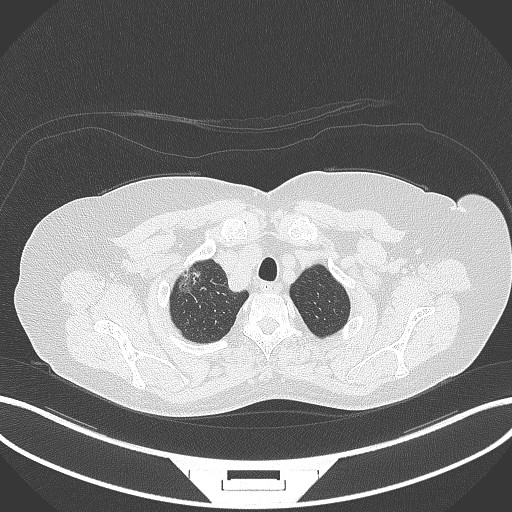
Chest CT, one axial slice; slice 315 of 365 in the series (ordered by position); reconstruction kernel B70f; 120 kVp; lung window (W 1500 / L -600 HU); 1 mm slice thickness; 512 × 512 image matrix, field of view 400 × 400 mm. Female patient, age 62 years. From the clinical record (not read from this slice): clinical TNM (as recorded): T1c N0 M0.
Annotated regions visible in this slice (bounding box drawn by a radiologist):
- lung tumour (recorded histology: adenocarcinoma): bounding box [x1, y1, x2, y2] px = [173, 258, 207, 295]